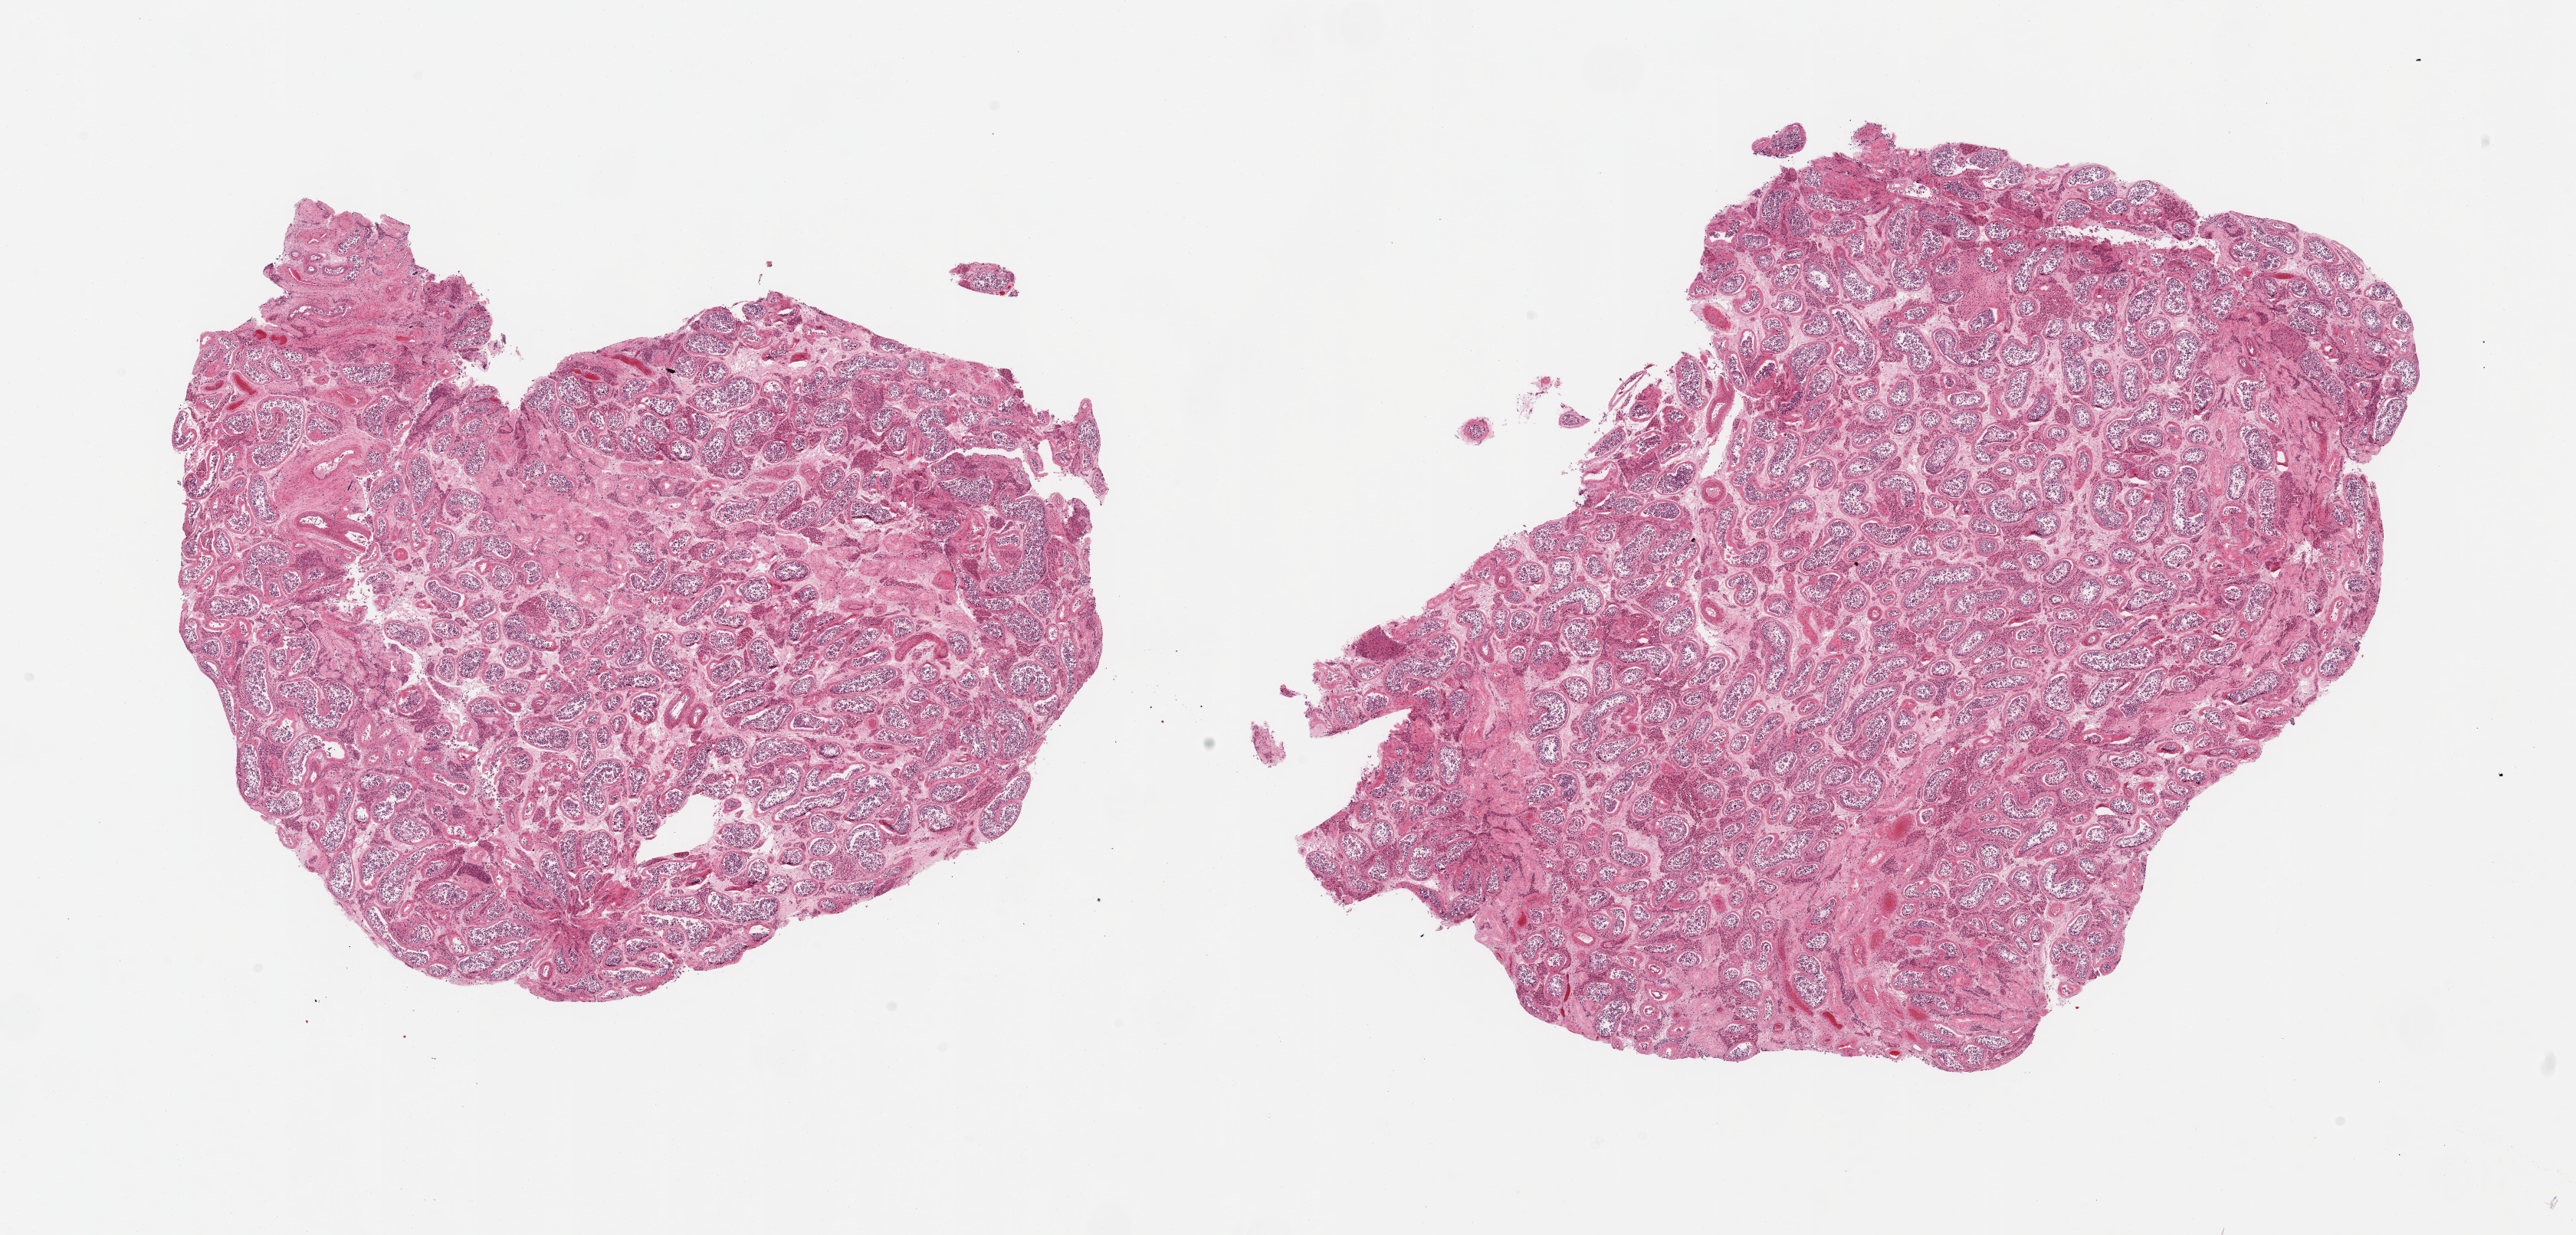
Digitized H&E-stained section — low-resolution overview of the scanned area, about 26.6 x 12.7 mm (slide scanned at 20x). PAXgene-fixed paraffin-embedded (PFPE) section. Target tissue: testis. Tissue donor sample. Donor sex: male.
* reviewer comment on this tissue sample: 2 pieces; atrophy with hyalinized tubules, increased Leydig cells